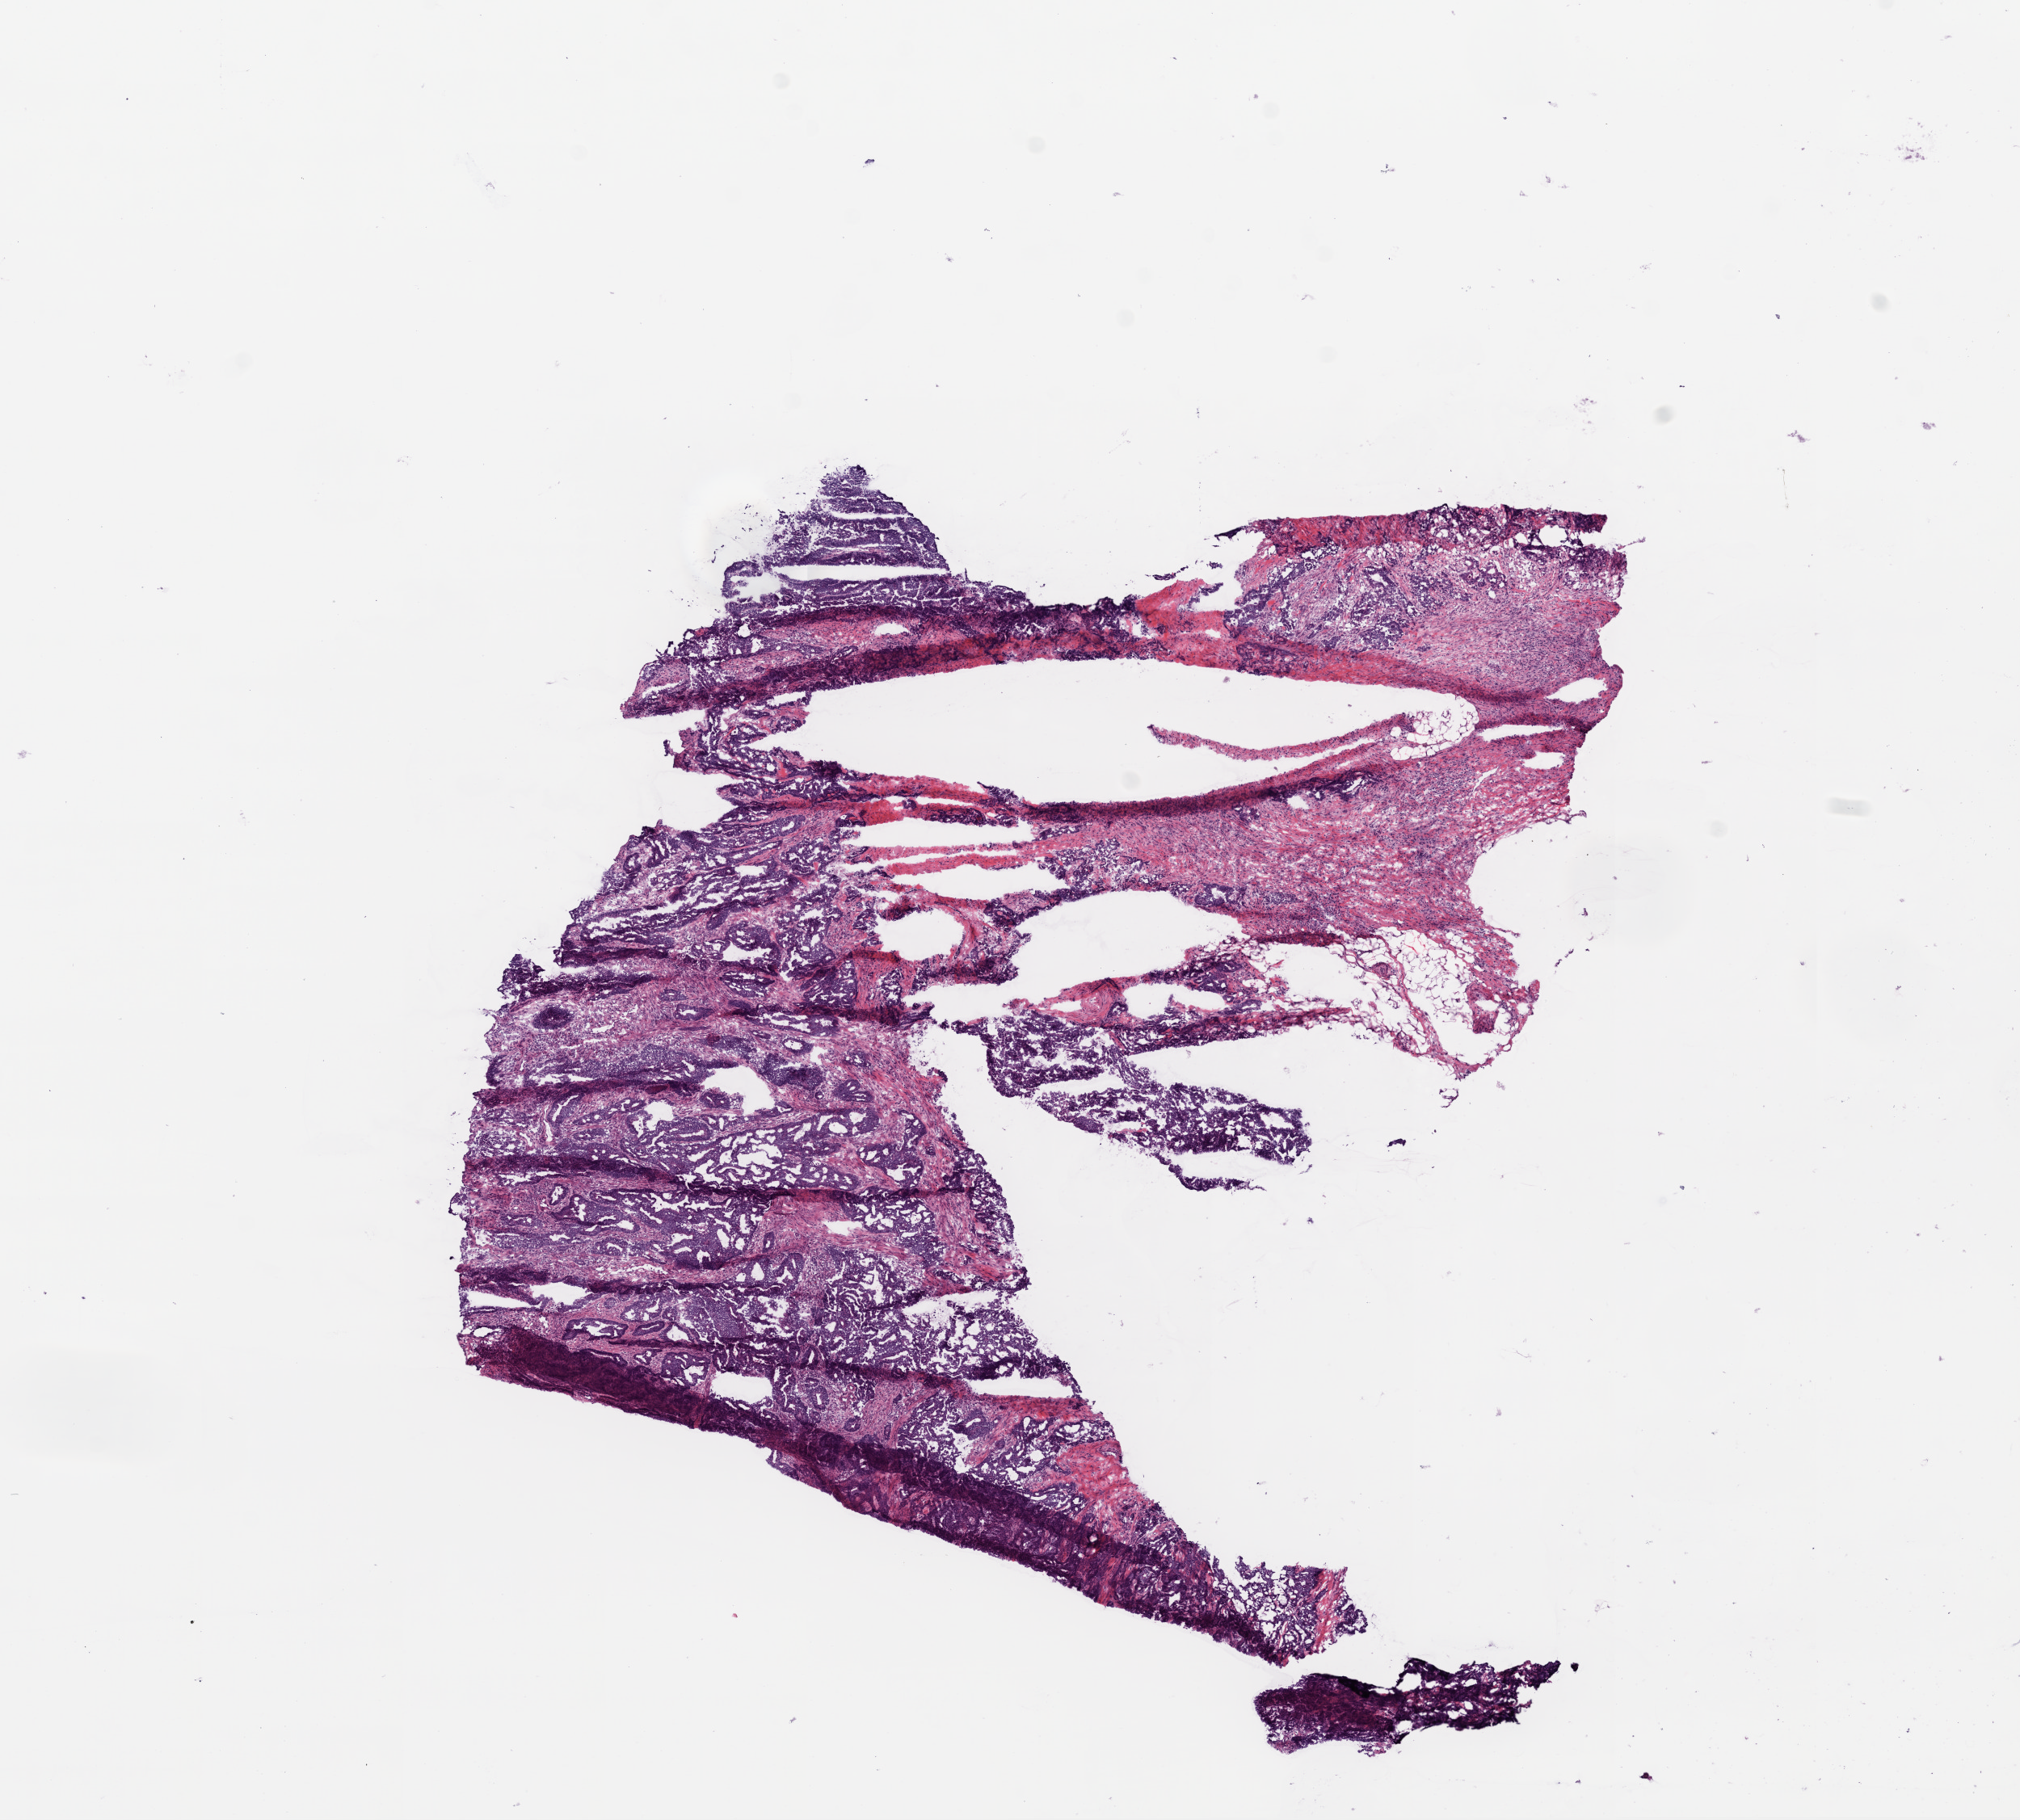
Digitized H&E tissue section (whole slide) — a low-resolution overview of the entire scanned area, about 10.0 x 9.0 mm (from a 20x scan), frozen section, primary tumour sample from the colon. Male patient; age at initial diagnosis 69 years. Slide review estimates, as recorded: tumour cells 90%, tumour nuclei 90%, normal cells 0%, stromal cells 5%, necrosis 5%.
Pathologic diagnosis: Adenocarcinoma, NOS. AJCC pathologic stage: IV.